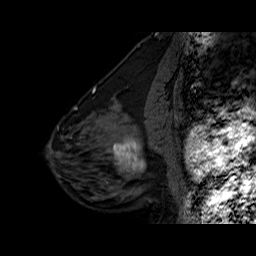
Breast MRI (dynamic contrast-enhanced), one sagittal slice. Position 24 of 60 along the scan axis. Dynamic contrast-enhanced series, time point 2 of 6 at this slice position (early post-contrast). 1.5 T. TE 6.3 ms, TR 32.5 ms. 256 × 256 image matrix. Female patient. From the clinical record (not read from this slice): setting: breast cancer imaged before/during neoadjuvant chemotherapy; receptor status: triple-negative.
Structures marked on this image (semi-automatically segmented with operator editing):
- analysis volume of interest (the breast-tissue region the enhancement analysis was run in; not a lesion): bounding box (x1, y1, x2, y2) in pixels: (102, 127, 162, 186)
- tumour enhancement mask (voxels above the 100 % enhancement threshold inside the analysis volume of interest): (113, 138, 144, 174)